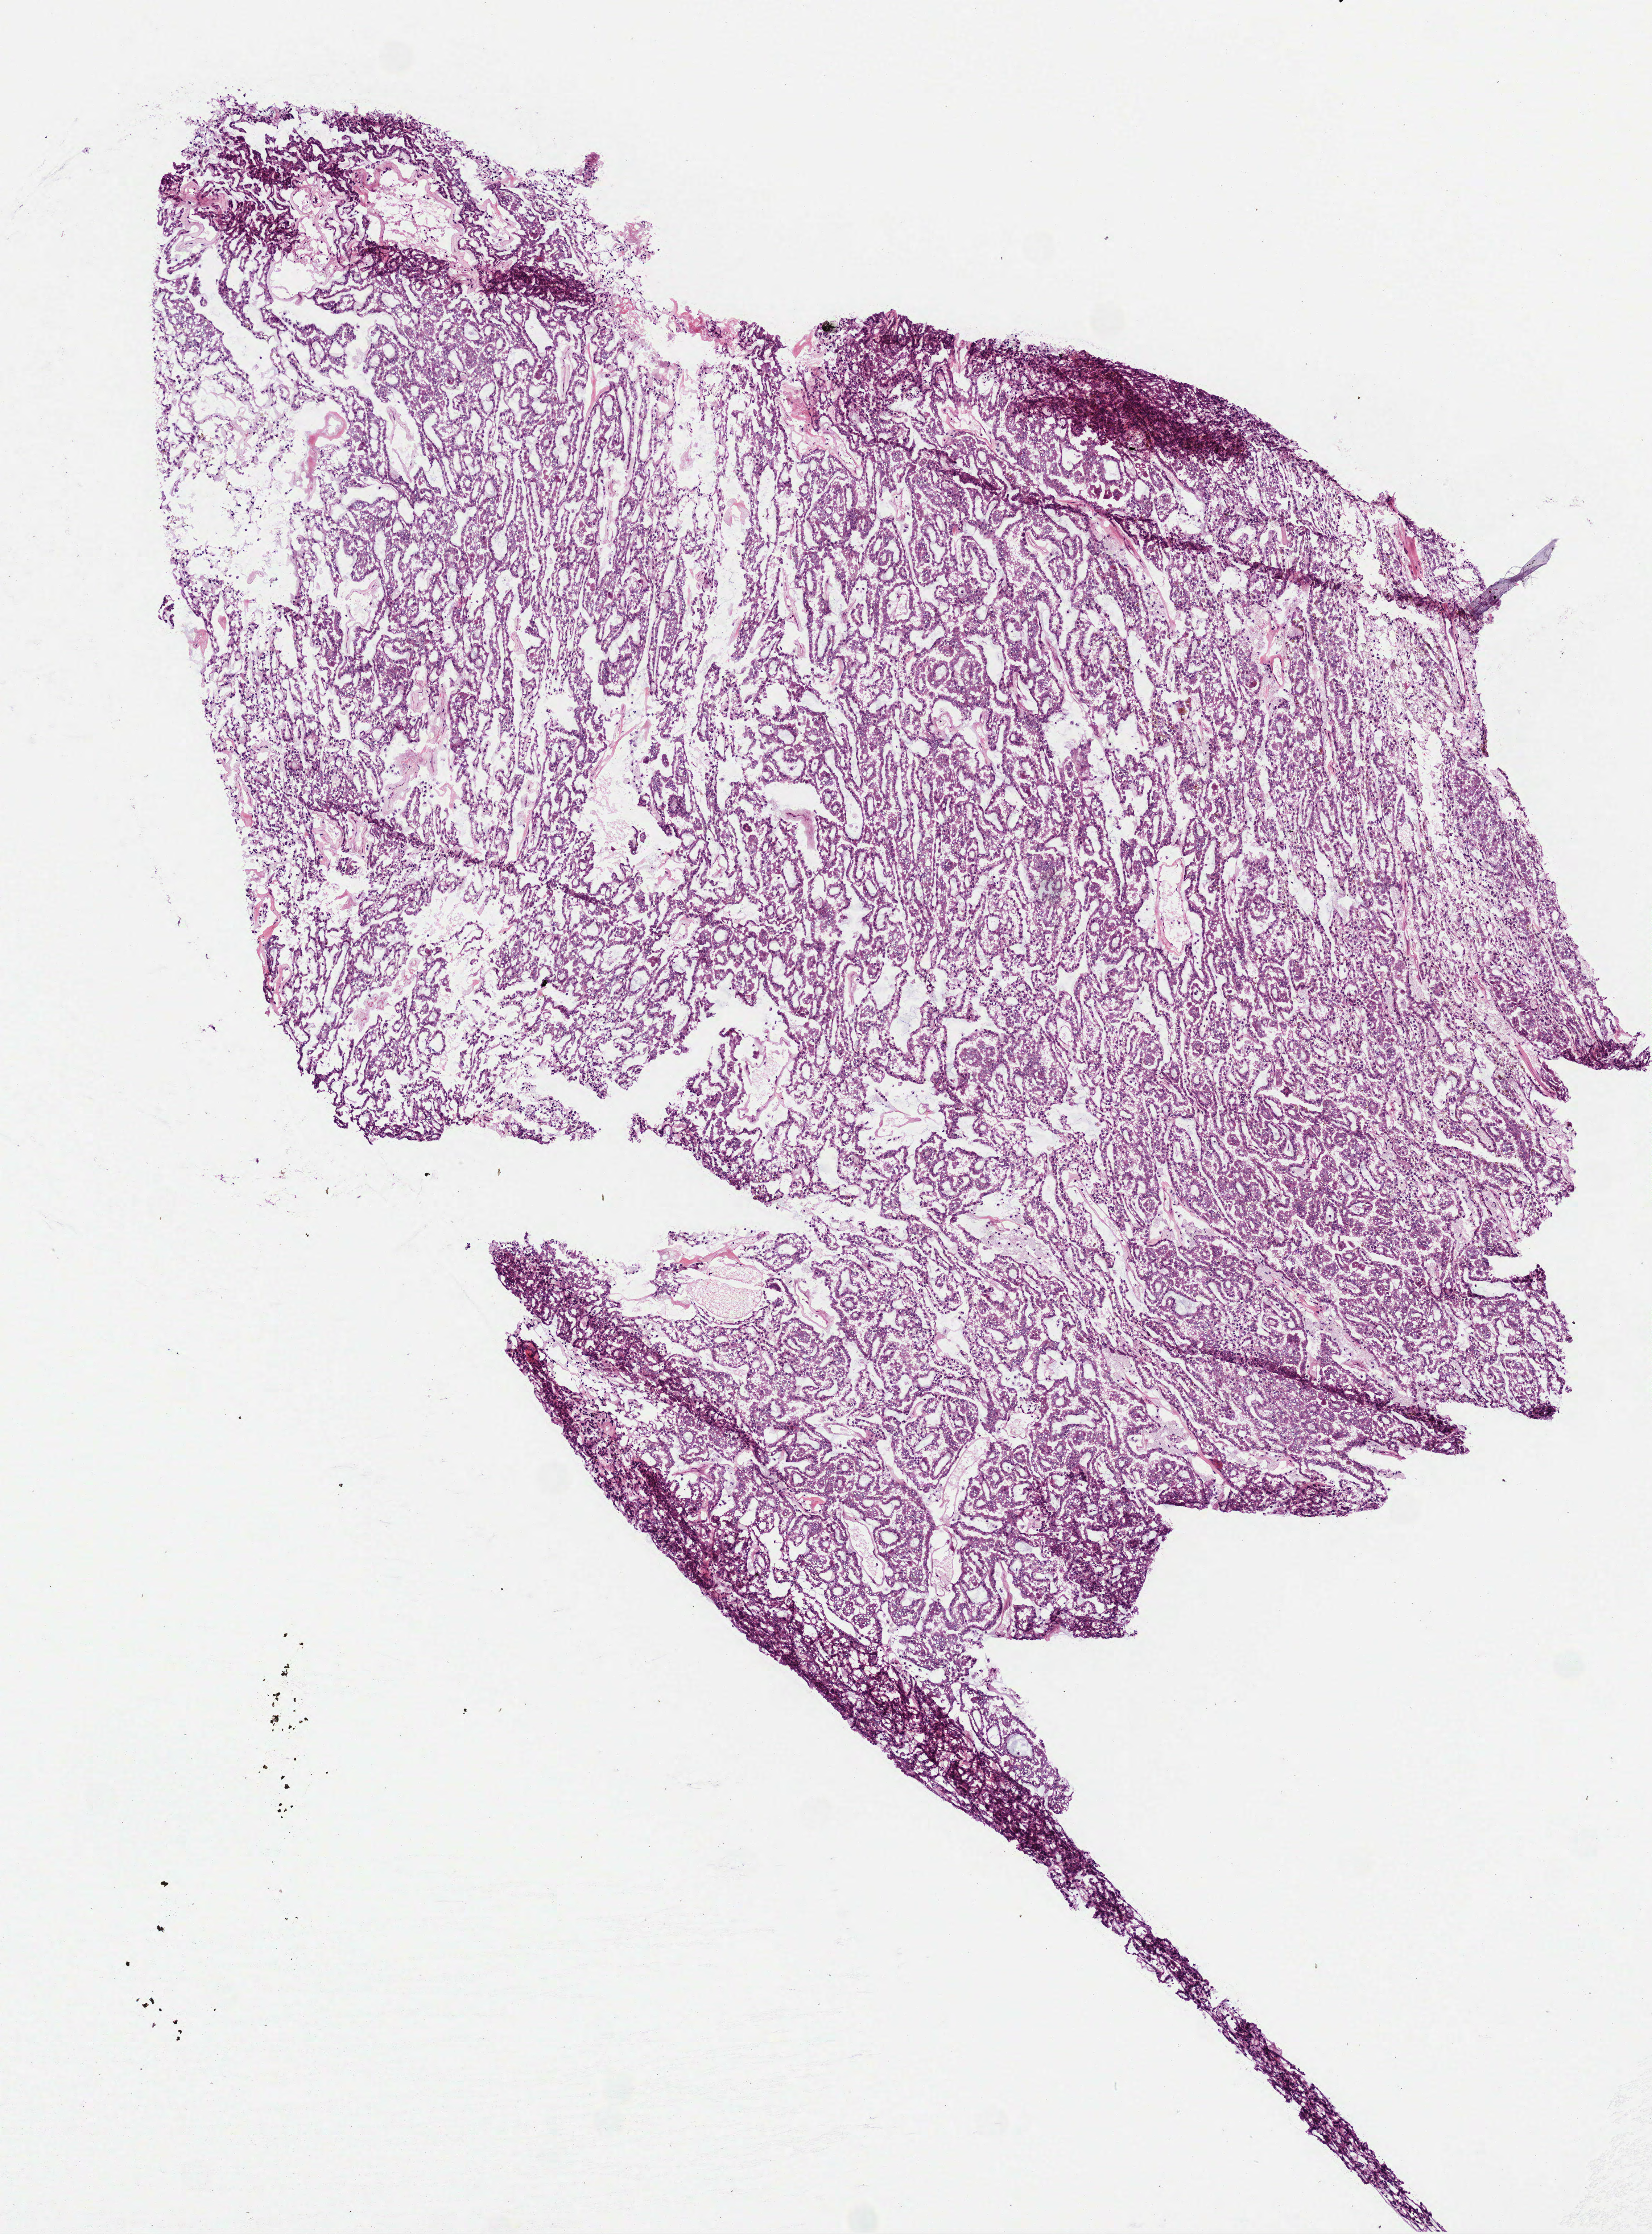
H&E-stained whole-slide image — a low-resolution overview of the entire scanned area, about 4.6 x 6.2 mm; frozen section; kidney, primary tumour sample. Patient sex: male.
Pathologic diagnosis: Papillary adenocarcinoma, NOS.